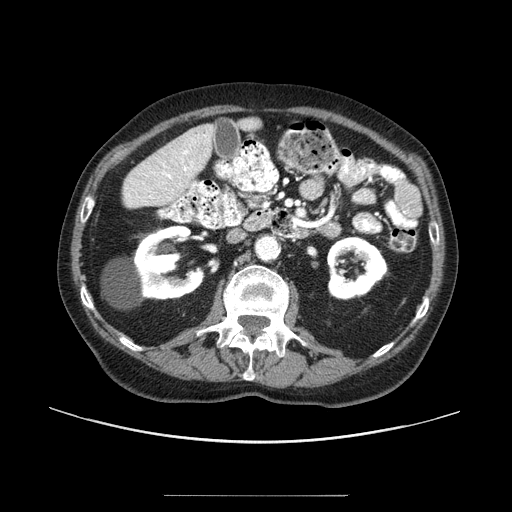
Contrast-enhanced abdominal CT (liver protocol), one axial slice; slice 32 of 91 in the series (ordered by position); 100 kVp; one of 2 acquisitions stored at this slice position; soft-tissue window (W 400 / L 40 HU); 512 × 512 image matrix, field of view 400 × 400 mm. From the clinical record (not read from this slice): diagnosis: hepatocellular carcinoma (patient treated with transarterial chemoembolisation; whether this scan precedes or follows treatment is not stated here); TNM stage (as recorded): Stage-I; Child-Pugh class: A; tumour differentiation: moderately differentiated; tumour nodularity: uninodular.
Outlined on this slice (semi-automatic segmentation, software-assisted and operator-edited):
- liver parenchyma outside the tumour (the mass and vessels are separate outlines, so this box may not span the whole liver): box from (x=124, y=124) to (x=216, y=206) px
- liver vessels: (x=150, y=135)–(x=208, y=199)